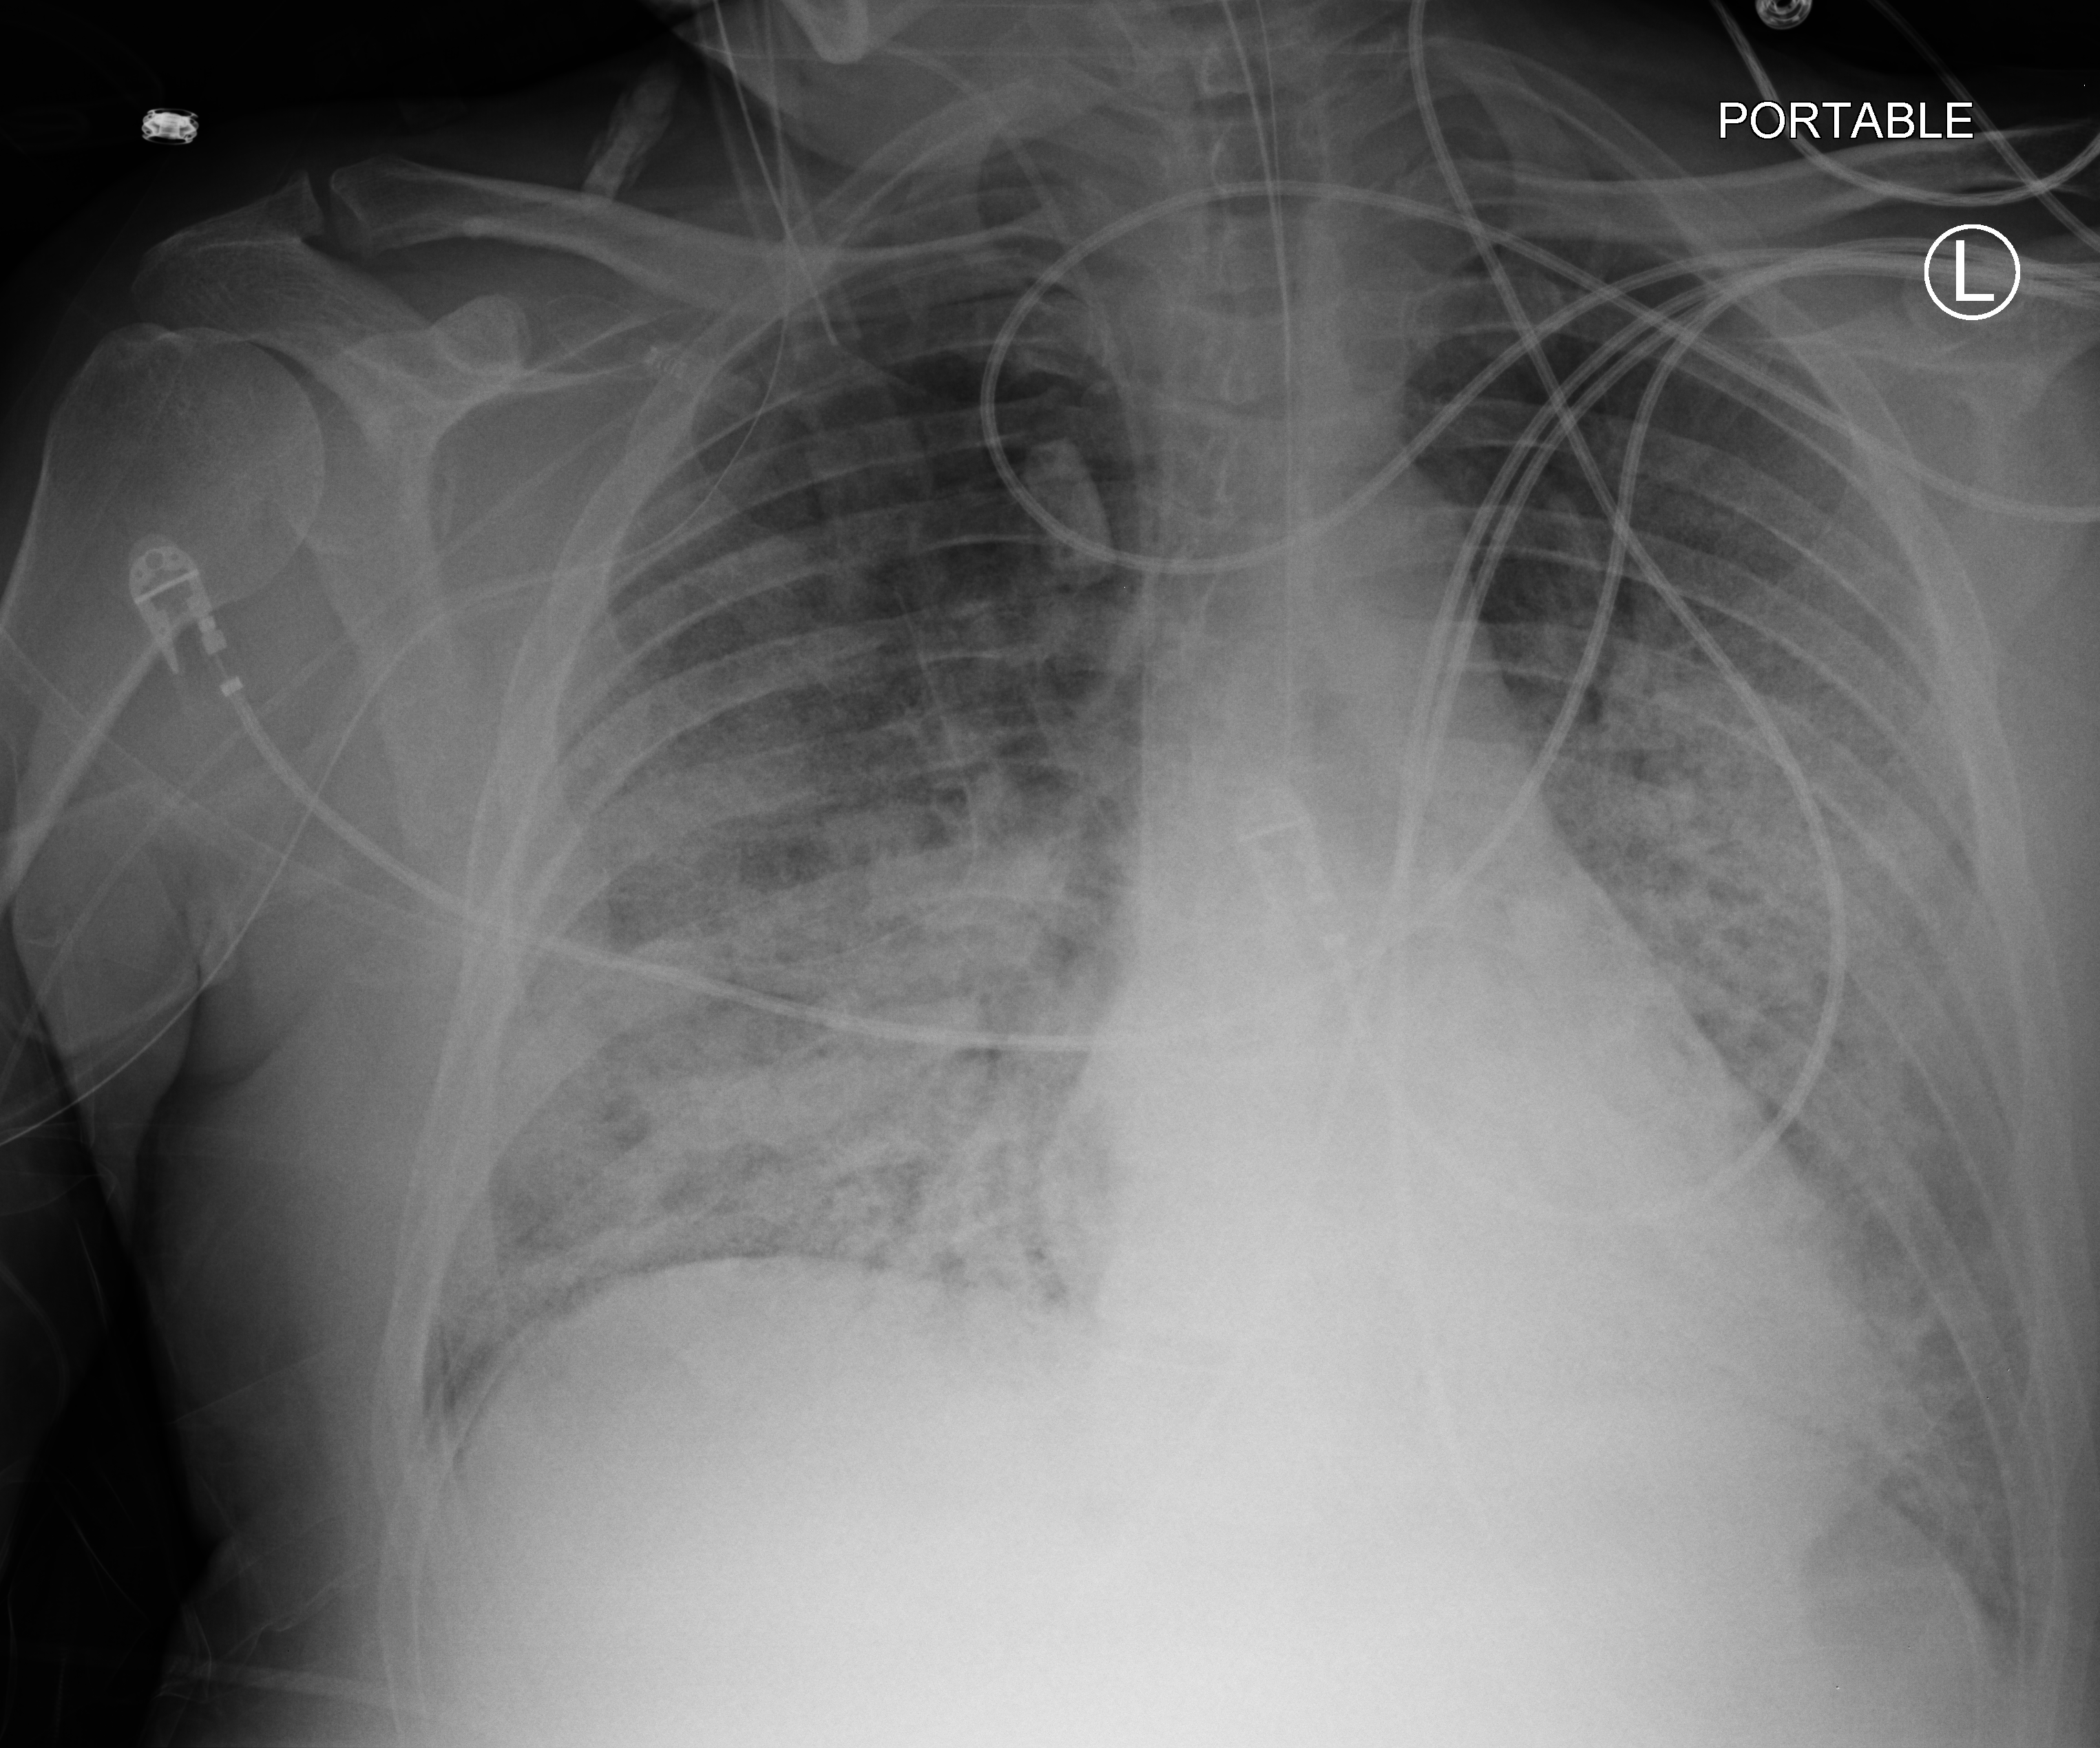
Chest X-ray (portable); anteroposterior (AP) projection. Male patient hospitalised with COVID-19, age 18–59 years.
Admission-level facts for this patient (not findings on this image; timing relative to this image not recorded):
- mechanically ventilated during this hospital stay: yes